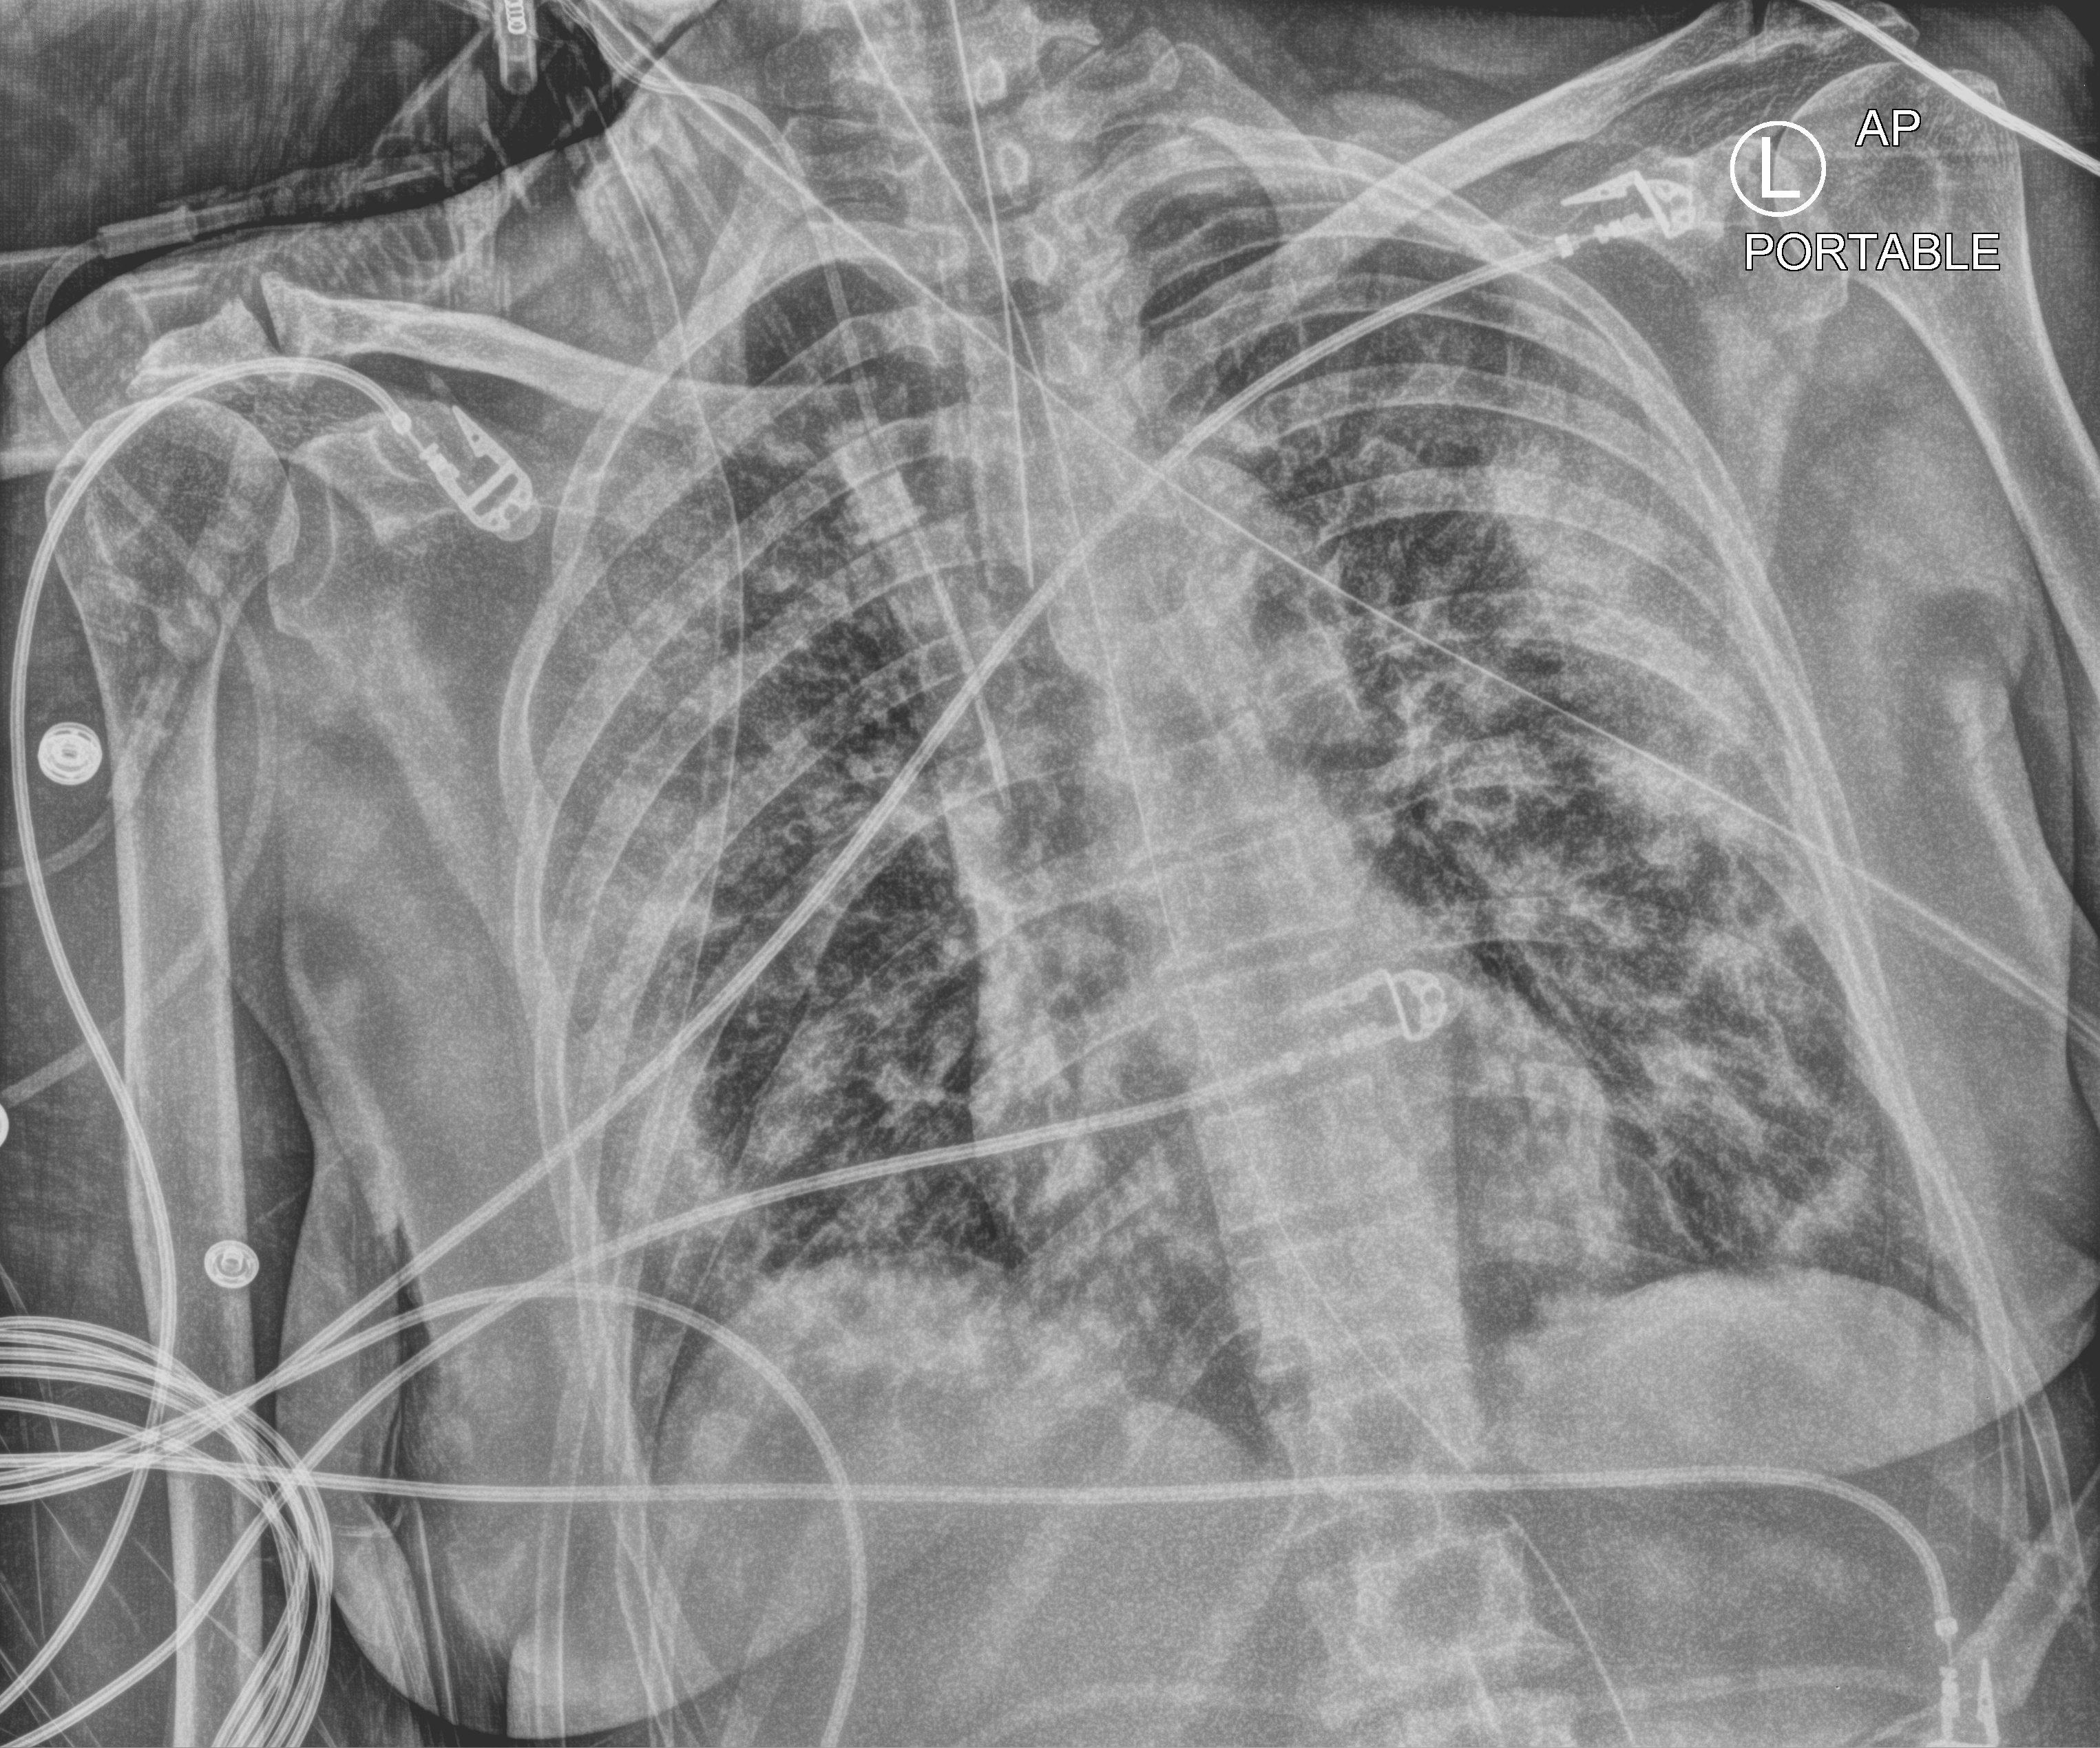
Portable chest radiograph, anteroposterior (AP) projection. Patient hospitalised with COVID-19; female, aged 60–74 years.
Hospital-stay facts (about this admission, not read from this image; timing relative to this image not recorded): COPD (admission record): no; length of hospital stay: 18 days; mechanically ventilated during this hospital stay: yes.